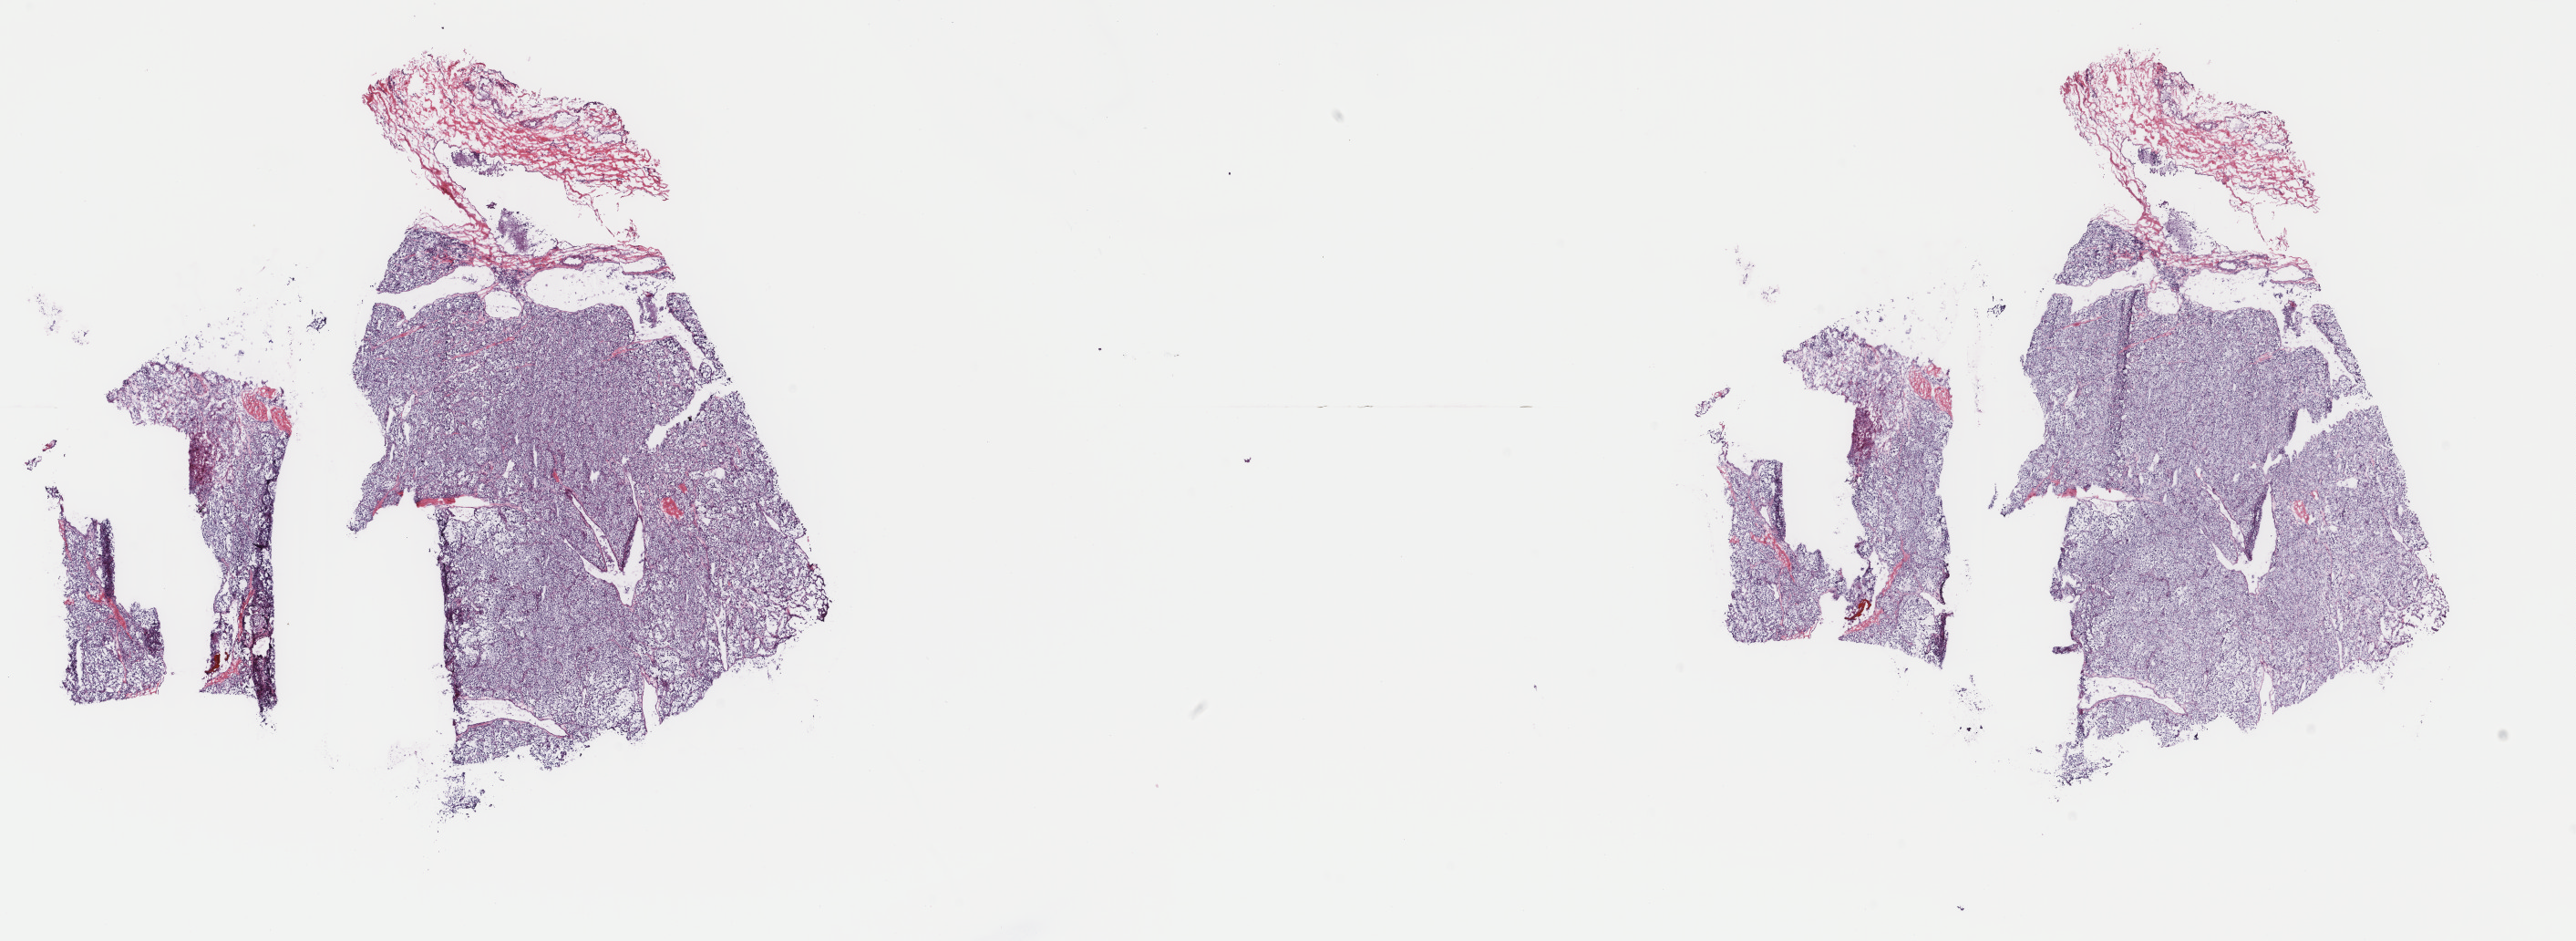
Whole-slide histology image, H&E — low-resolution overview of the scanned area, about 22.4 x 8.2 mm (acquisition: 40x scan), frozen section, metastatic tumour sample. Male patient; age at initial diagnosis 55 years. Pathologist review of this section (percent, as recorded): tumour cells 95%, tumour nuclei 80%, normal cells 5%, stromal cells 0%, necrosis 0%. Infiltration values recorded for this section: lymphocyte infiltration 1%, monocyte infiltration 0%, neutrophil infiltration 0%.
This section: metastatic tumour tissue. Patient diagnosis: Paraganglioma, malignant (primary site: nervous system, NOS).